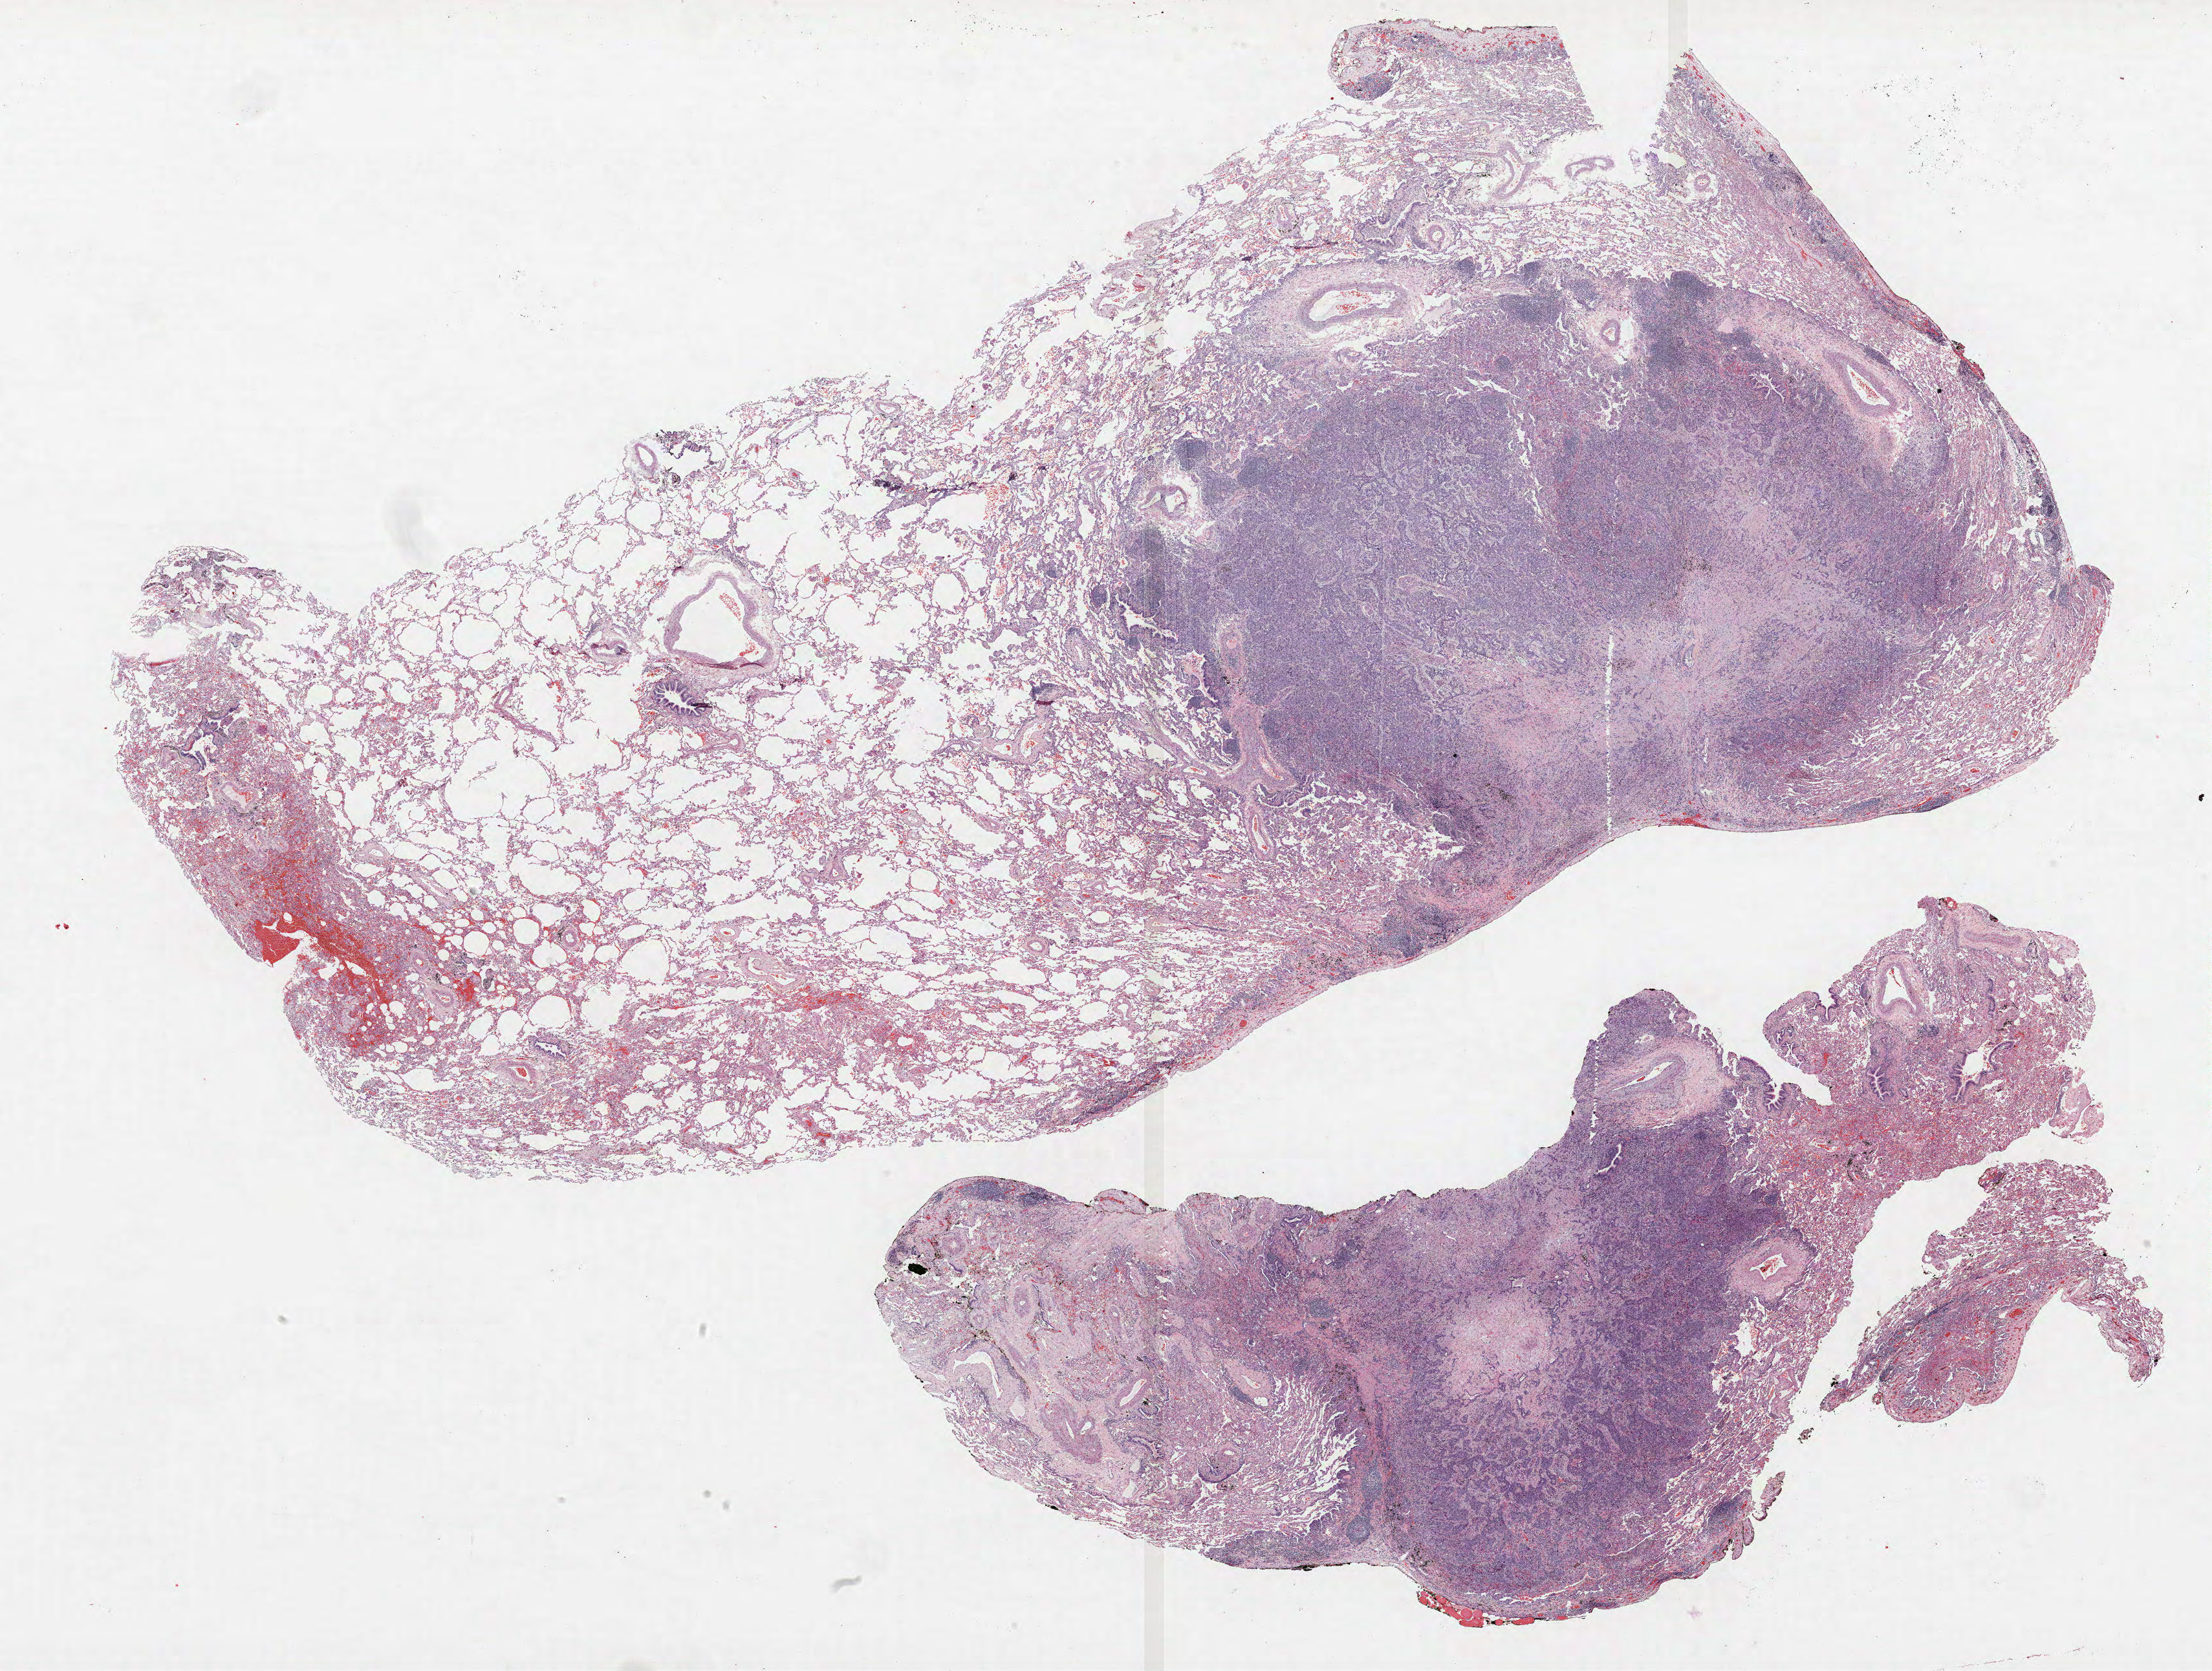
Whole-slide histology image, Hematoxylin and eosin (H&E) stained — low-resolution overview of the scanned area, about 27.4 x 20.7 mm, formalin-fixed paraffin-embedded (FFPE) section, lung tissue. Male patient, aged 62 at enrolment. Former smoker at enrolment. Grade: poorly differentiated (G3).
Primary tumour location (clinical record): right lower lobe. Stage (AJCC 6th edition): IV. Tumour size (pathology): 15 mm. Participant's lung-cancer diagnosis: Adenocarcinoma, NOS.